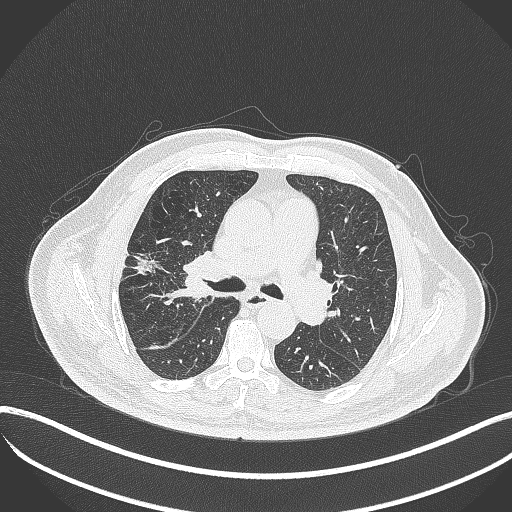
Chest CT, one axial slice; slice 221 of 401 in the series (ordered by position); reconstruction kernel B70f; lung window (W 1500 / L -600 HU); 1 mm slice thickness; 512 × 512 image matrix, field of view 400 × 400 mm. Patient: male, 72 years. Case-level facts recorded for this patient, not image findings: clinical TNM (as recorded): T1c N0 M0; histopathological grade: G2.
Outlined on this slice (rectangle marked by the reading radiologist):
- lung tumour (recorded histology: squamous cell carcinoma): box from (x=165, y=247) to (x=202, y=305) px